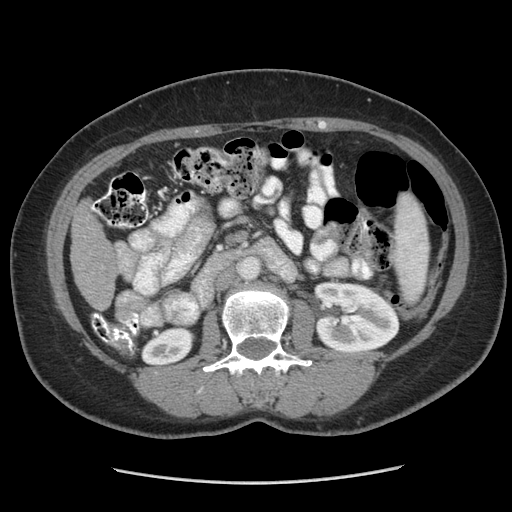
Contrast-enhanced abdominal CT (liver protocol), one axial slice. Position 118 of 185 along the scan axis. 140 kVp. Soft-tissue window (W 400 / L 40 HU). 512 × 512 image matrix, field of view 360 × 360 mm. Case-level facts recorded for this patient, not image findings: diagnosis: hepatocellular carcinoma (patient treated with transarterial chemoembolisation; whether this scan precedes or follows treatment is not stated here); TNM stage (as recorded): Stage-I.
Structures marked on this image (semi-automatically segmented with operator editing):
- liver parenchyma outside the tumour (the mass and vessels are separate outlines, so this box may not span the whole liver): box from (x=70, y=202) to (x=118, y=308) px